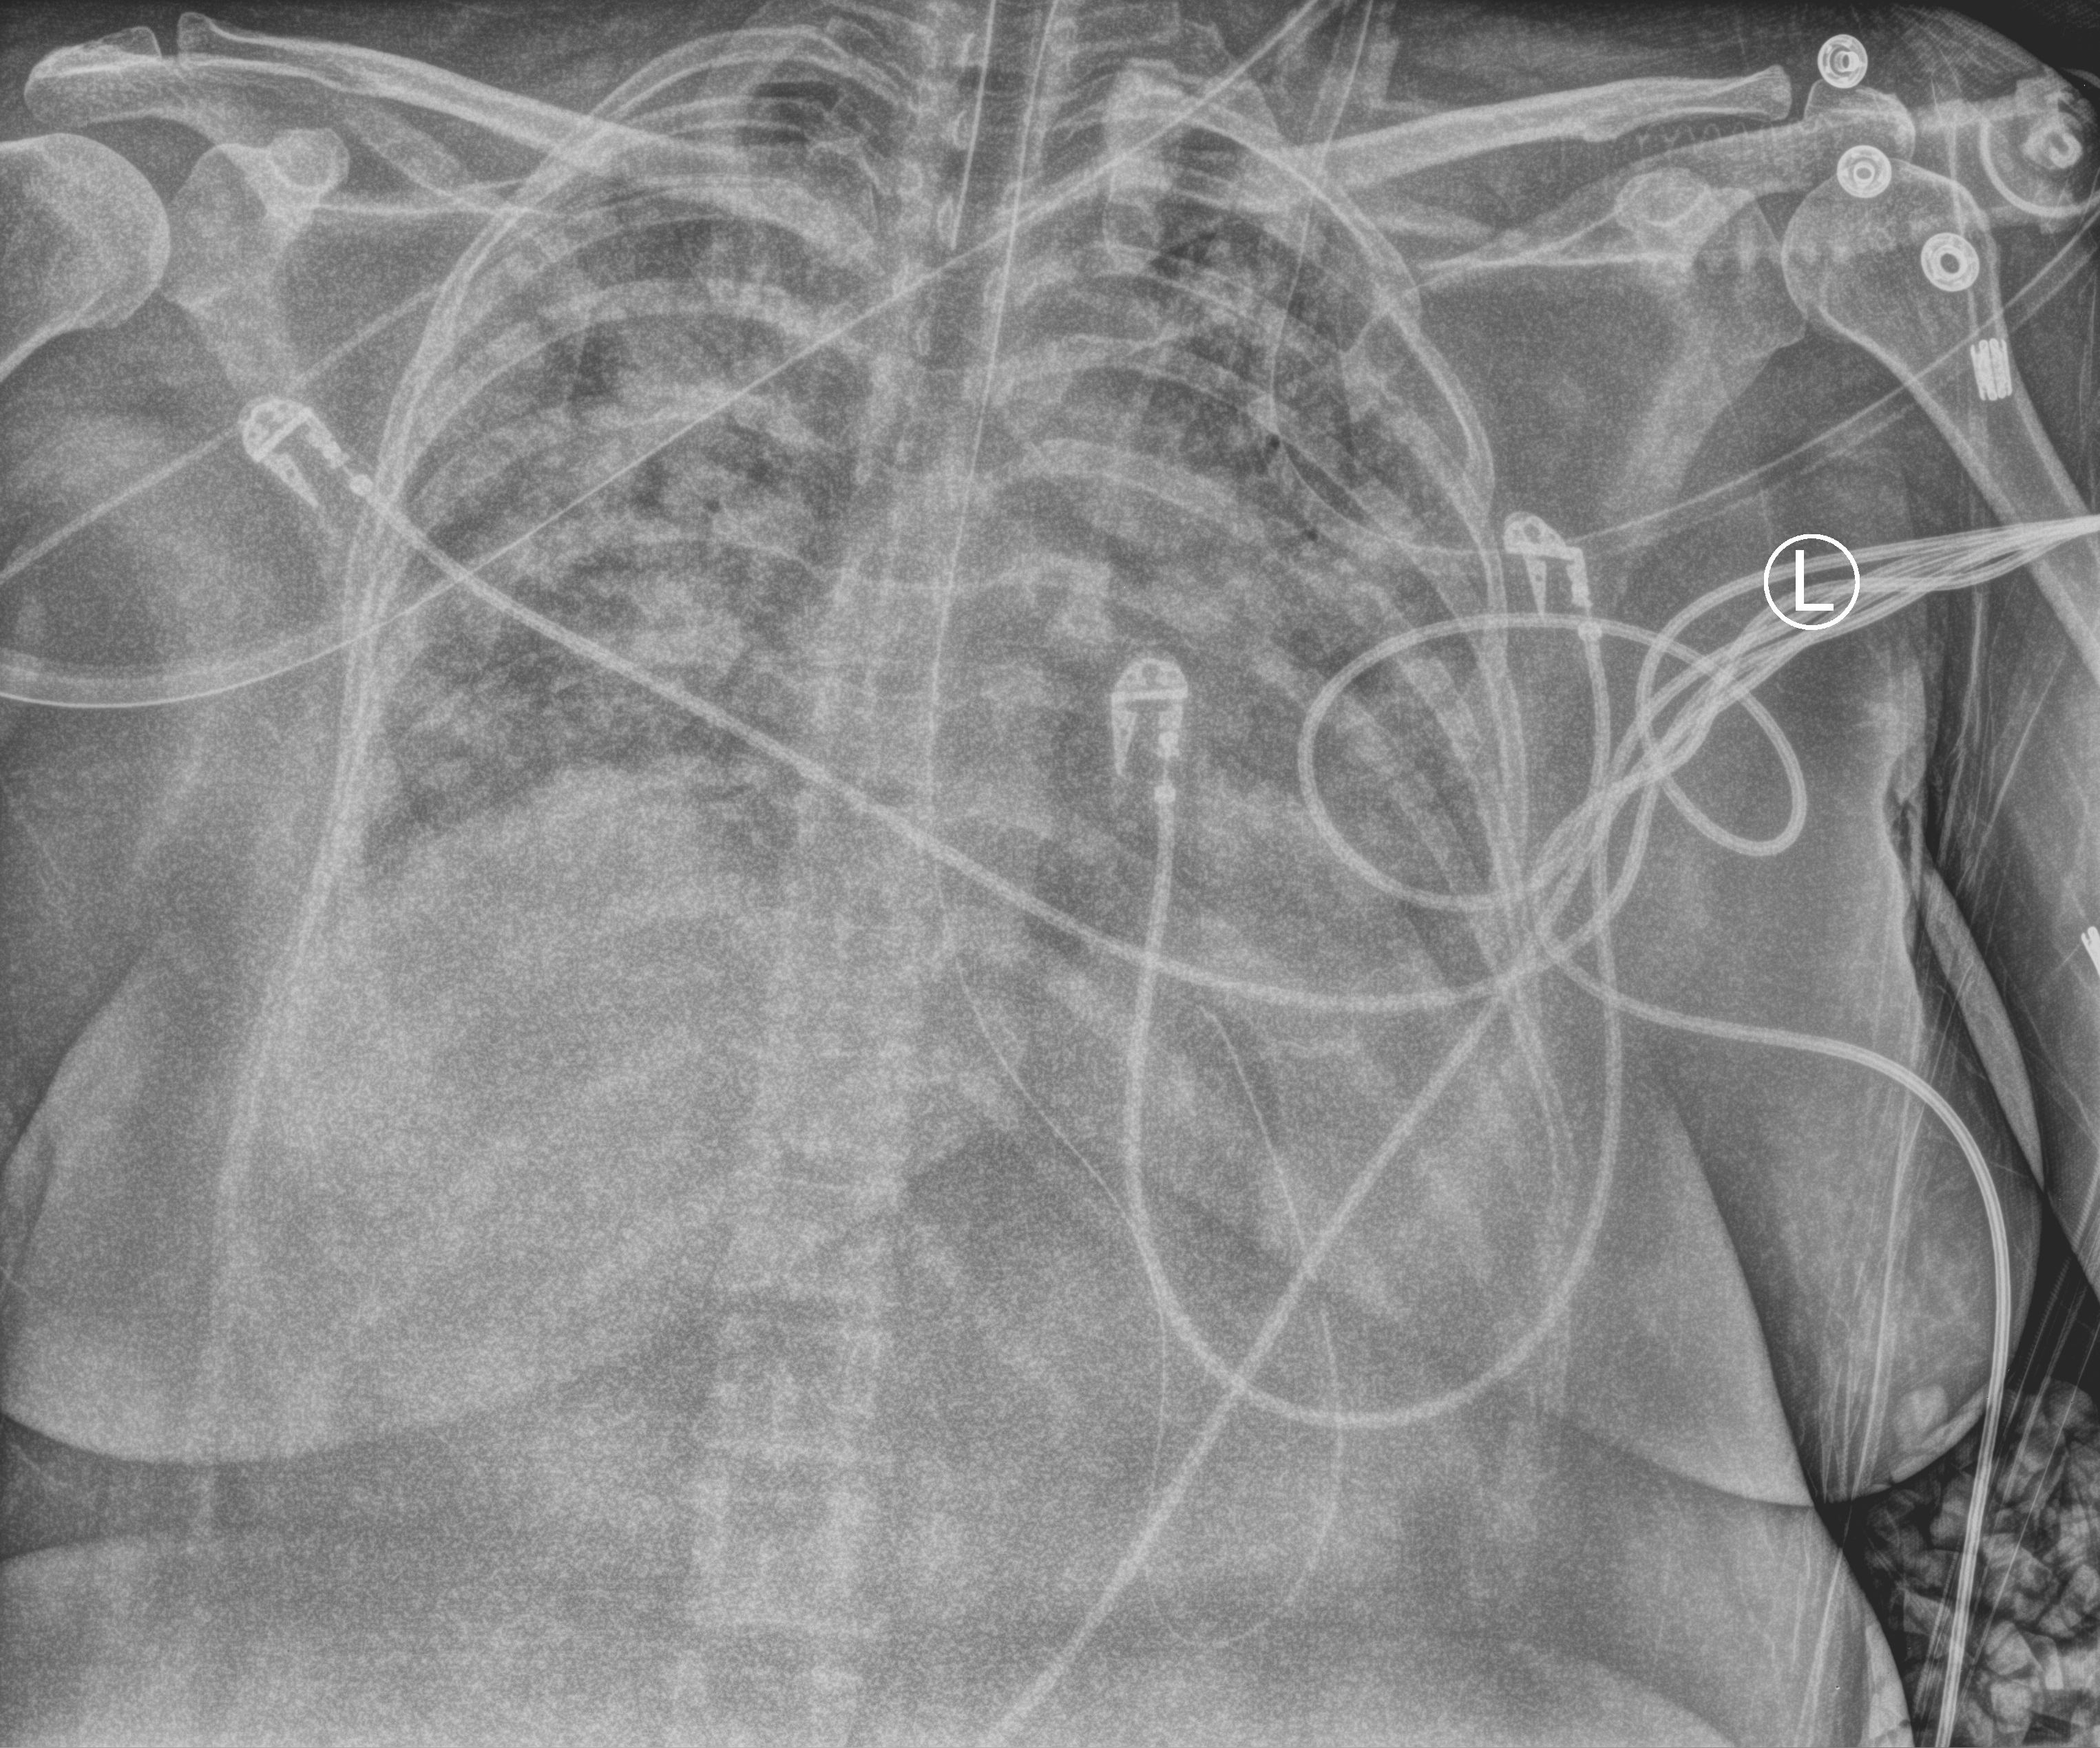
Portable chest radiograph. Adult patient hospitalised with COVID-19, age 18–59 years.
From the hospital-stay record, not from the radiograph (when in the stay this image was taken is not recorded): mechanically ventilated during this hospital stay: yes; other chronic lung disease (admission record): yes; admitted to intensive care during this hospital stay: yes.